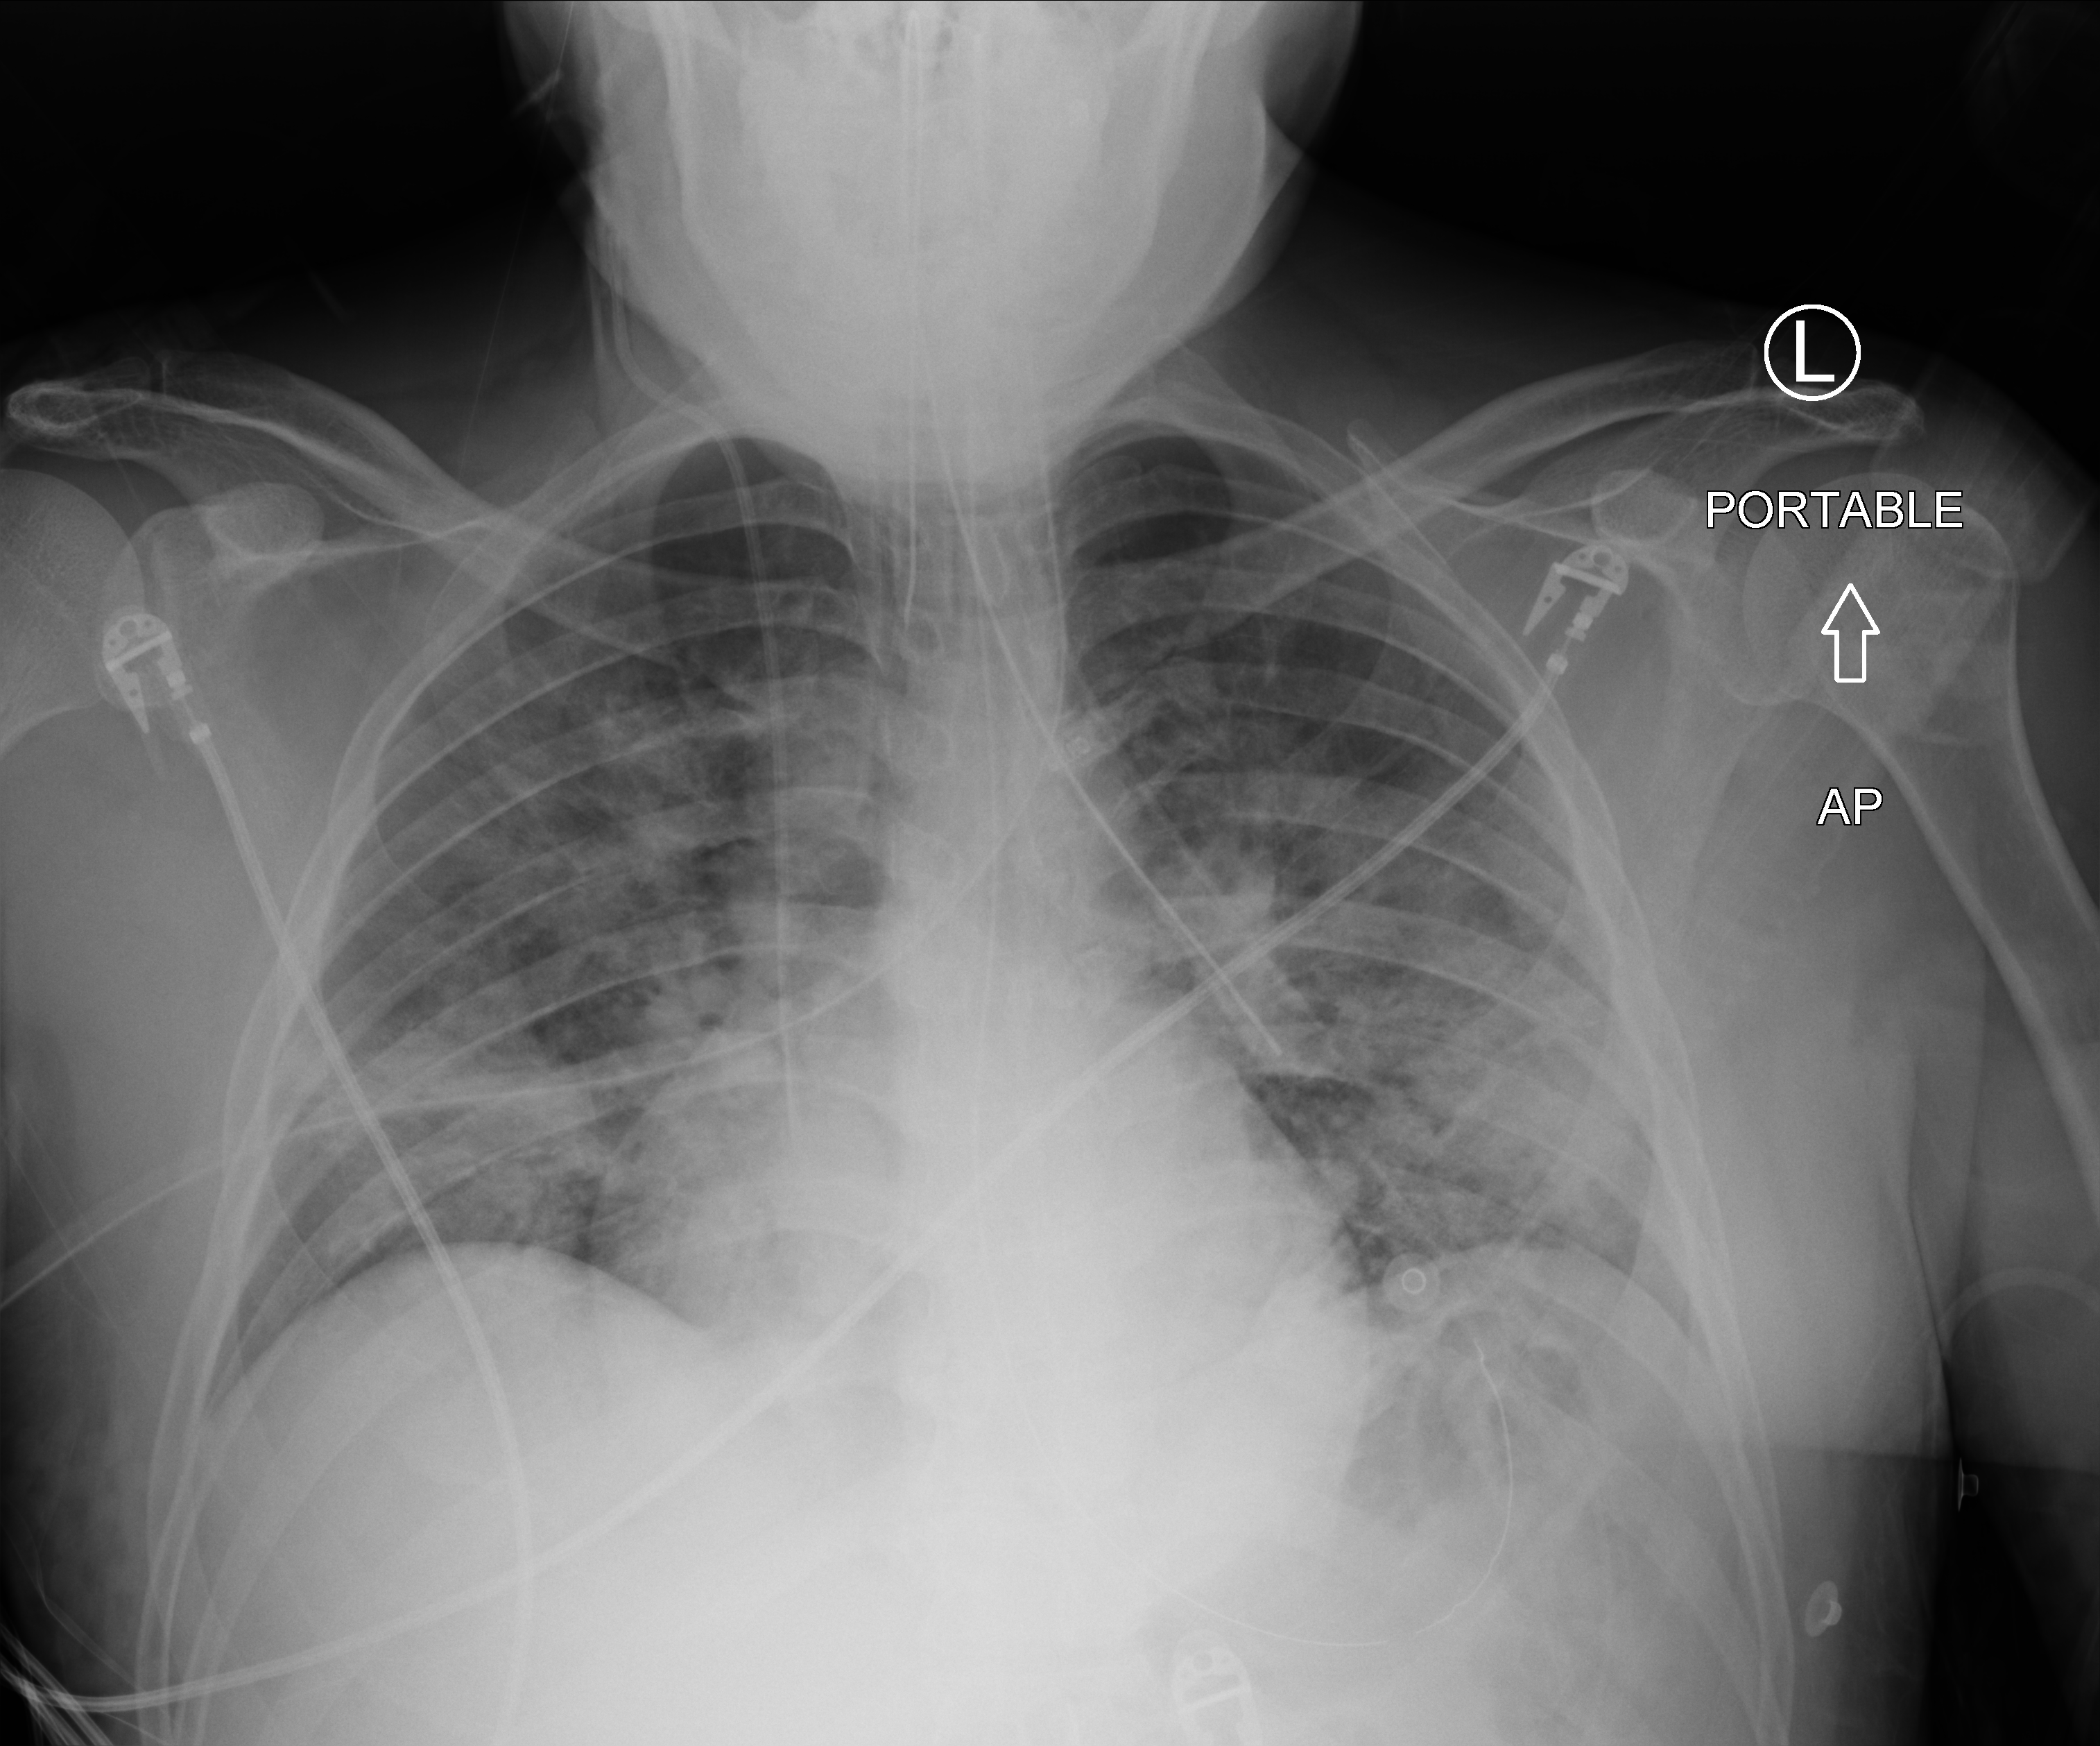
Bedside chest radiograph (computed radiography); anteroposterior (AP) projection. Male patient hospitalised with COVID-19, age 18–59 years.
Hospital-stay facts (about this admission, not read from this image; timing relative to this image not recorded): diabetes (admission record): no.